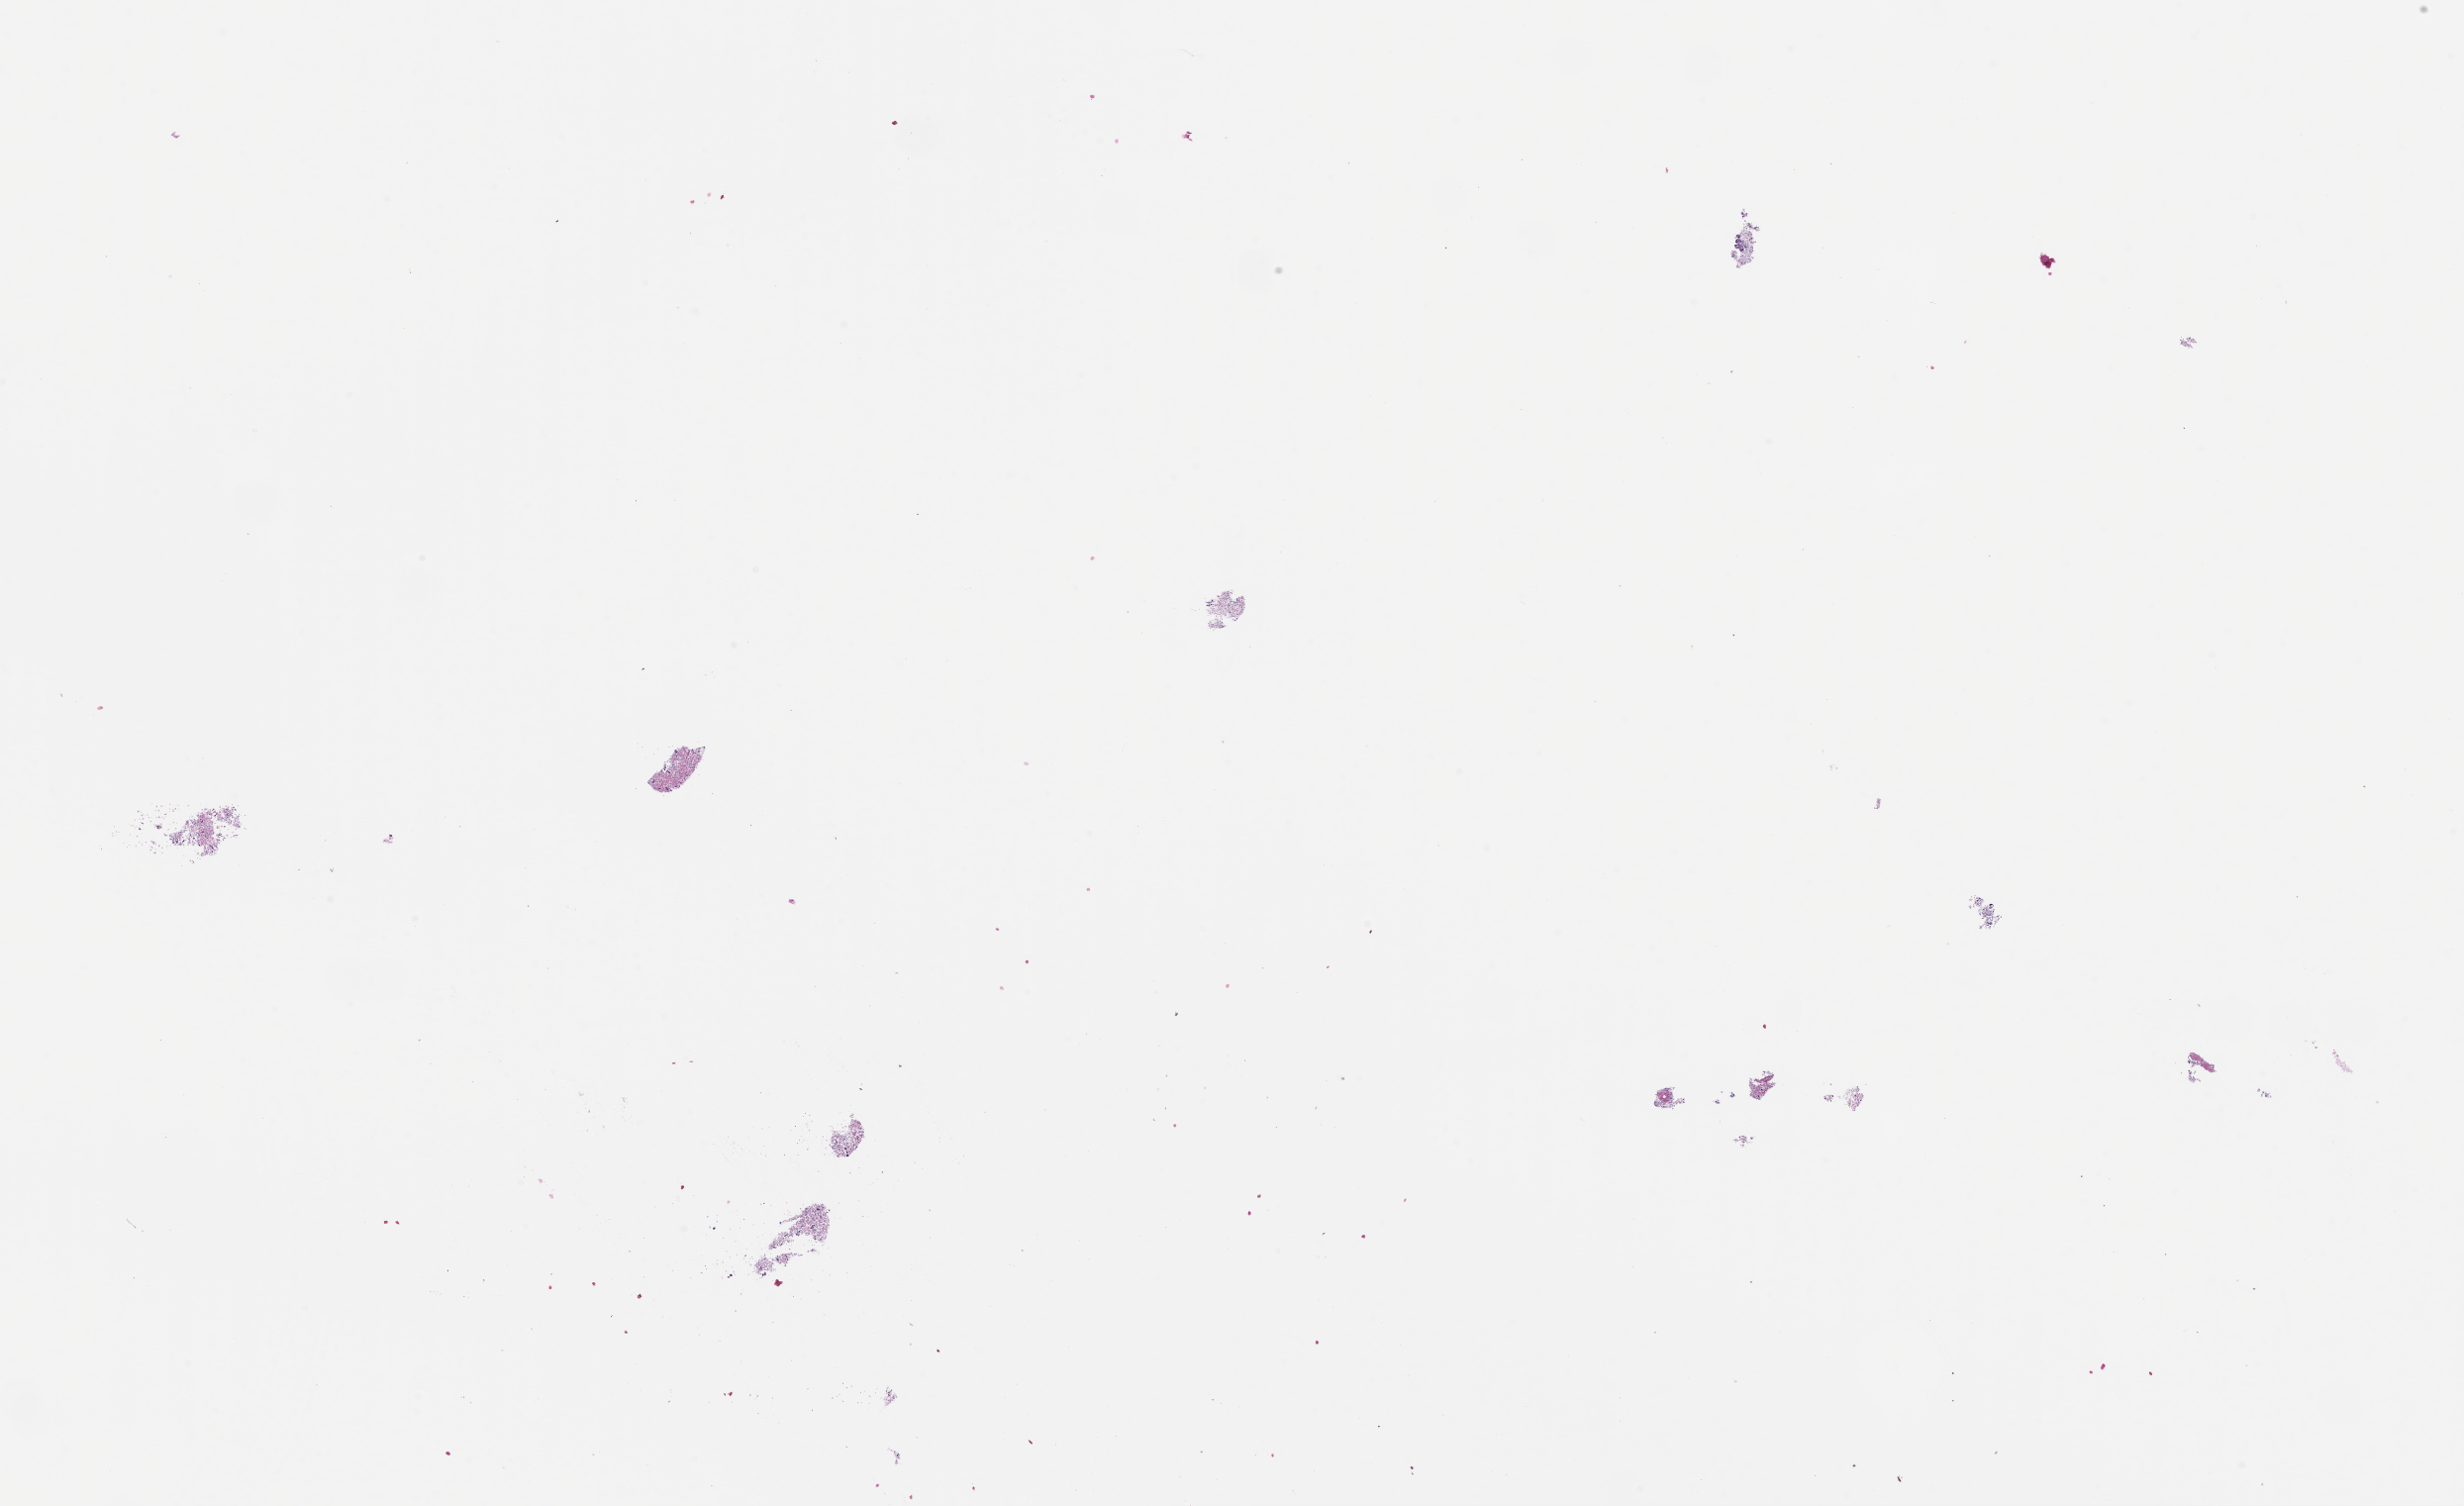
H&E whole-slide image — a low-resolution overview of the entire scanned area, about 20.1 x 12.3 mm; FFPE section; tissue site: lung; collected on treatment. Male patient.
This section: primary tumor. Diagnosis: Non-Small Cell Lung Carcinoma.